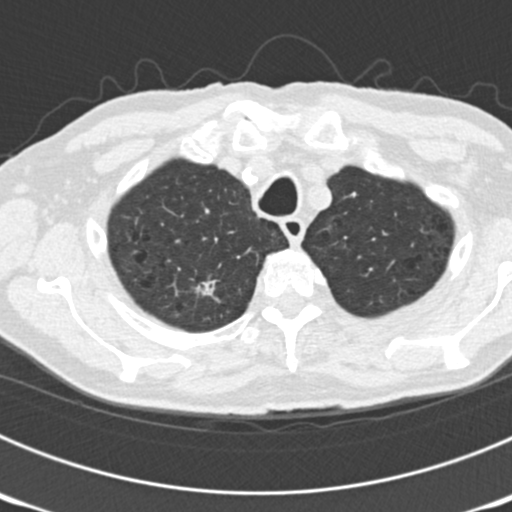
Low-dose screening chest CT, one axial slice. Position 154 of 177 along the scan axis. Reconstruction kernel B30f. 120 kVp. Lung window (W 1500 / L -600 HU). 2 mm slice thickness. 512 × 512 image matrix, field of view 300 × 300 mm.
Annotated regions visible in this slice (manually delineated by an expert):
- lesion 3 (nodule, upper lobe of right lung): bounding box [x1, y1, x2, y2] px = [196, 279, 221, 296]